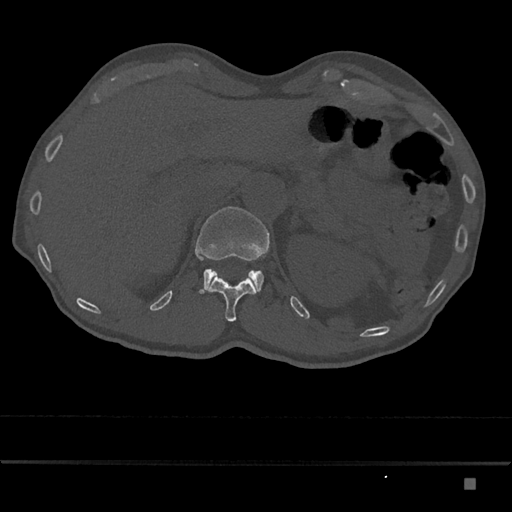
CT including the spine, one axial slice; position 583 of 797 along the scan axis; reconstruction kernel Br40s/3; bone window (W 1800 / L 400 HU); 512 × 512 image matrix. Patient: male, 72 years. Case-level facts recorded for this patient, not image findings: primary cancer: prostate.
Structures marked on this image (semi-automatically segmented with operator editing):
- L1 vertebra: box from (x=195, y=207) to (x=270, y=294) px
- T12 vertebra: (x=202, y=276)–(x=256, y=322)